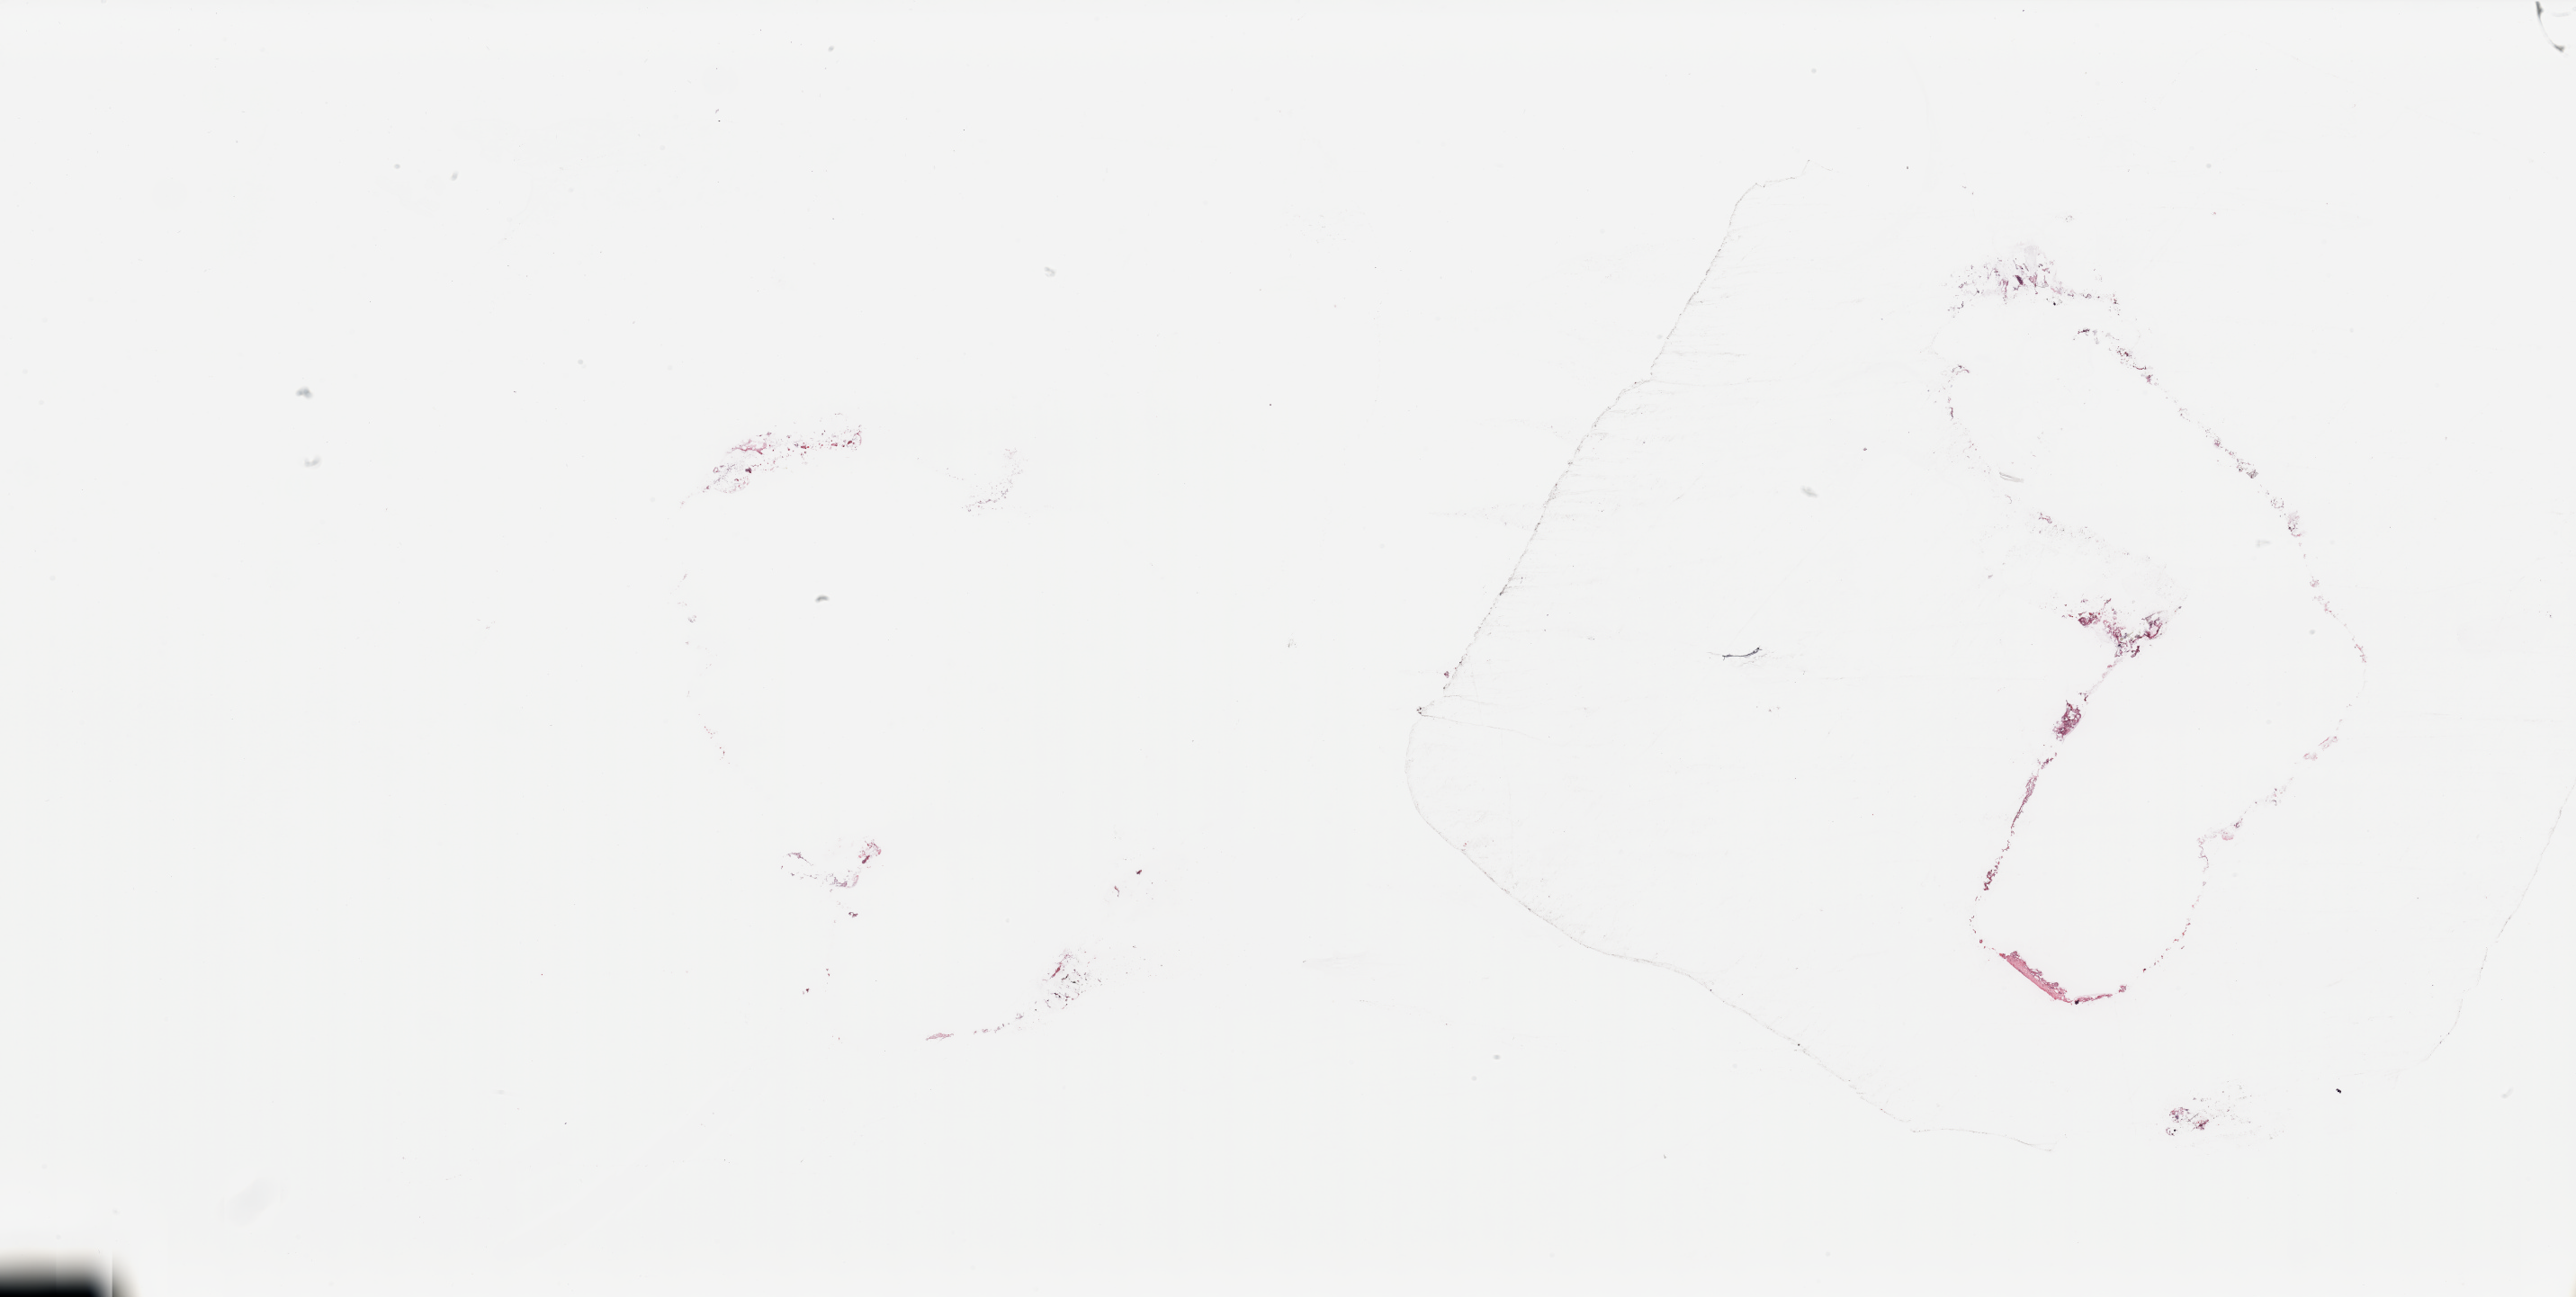
Digitized Hematoxylin and eosin (H&E) stained tissue section (whole slide) — low-resolution overview of the scanned area, about 45.3 x 22.8 mm (acquisition: 20x scan); breast, tissue type not recorded.
- patient diagnosis (cohort enrolment): breast cancer (breast)